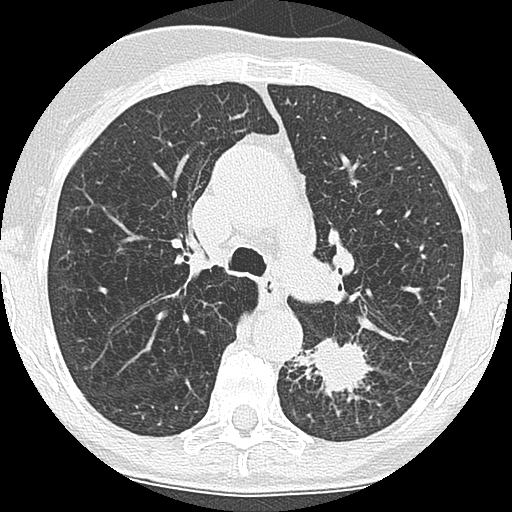
Low-dose screening chest CT, one axial slice. Slice 117 of 171 in the series (ordered by position). 120 kVp. Lung window (W 1500 / L -600 HU). 512 × 512 image matrix, field of view 280 × 280 mm.
Outlined on this slice (expert manual segmentation):
- lesion 1 (tumor, lower lobe of left lung): bounding box [x1, y1, x2, y2] px = [293, 338, 369, 392]